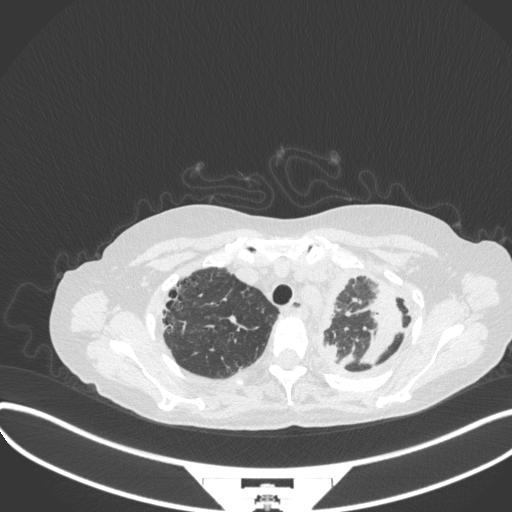
Chest CT, one axial slice. Position 280 of 373 along the scan axis. Reconstruction kernel B31f. Lung window (W 1500 / L -600 HU). 1 mm slice thickness. 512 × 512 image matrix, field of view 400 × 400 mm. Patient: female, 56 years. From the clinical record (not read from this slice): clinical TNM (as recorded): T1 N0 M0.
Structures marked on this image (bounding box drawn by a radiologist):
- lung tumour (recorded histology: adenocarcinoma): bounding box (x1, y1, x2, y2) in pixels: (360, 285, 406, 370)